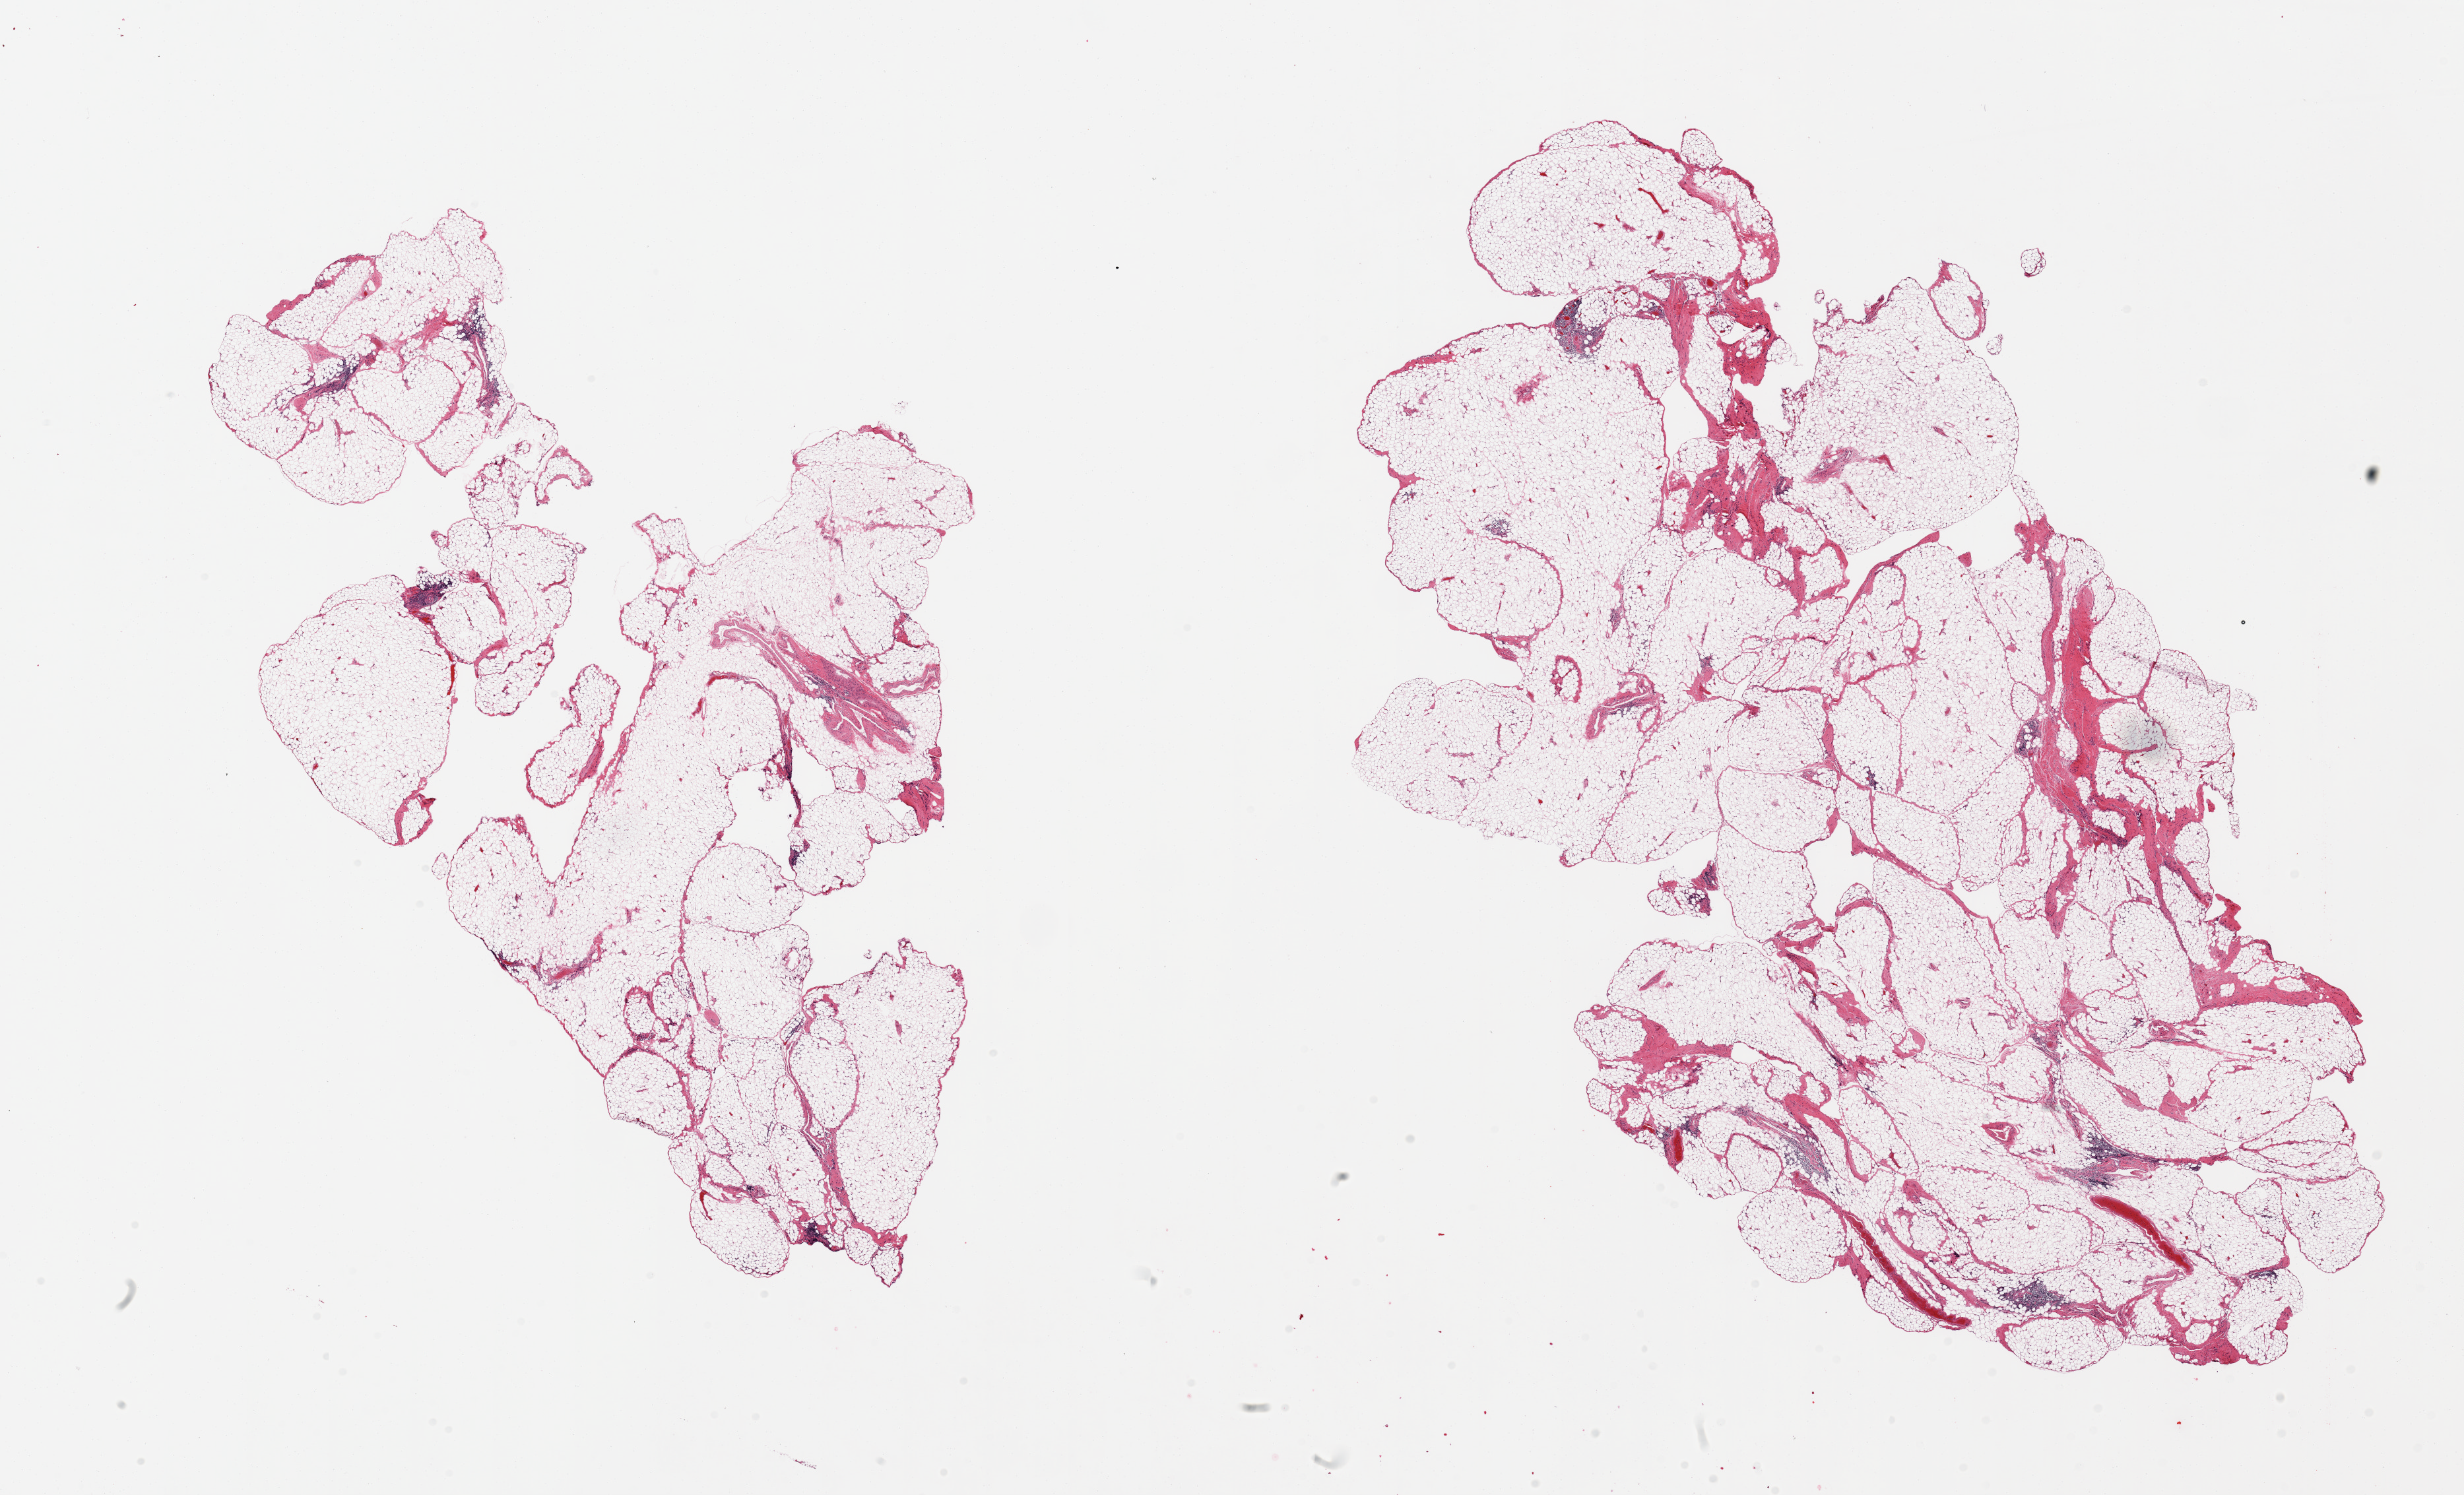
H&E whole-slide image — whole scanned area (about 29.5 x 17.9 mm) shown as a low-resolution overview; PAXgene-fixed, paraffin-embedded tissue; section of omentum (target tissue); donor tissue sample.
Reviewer comment on this tissue sample: 2 pieces, fibrosis/mesothelial hyperplasia, ~10-20%.